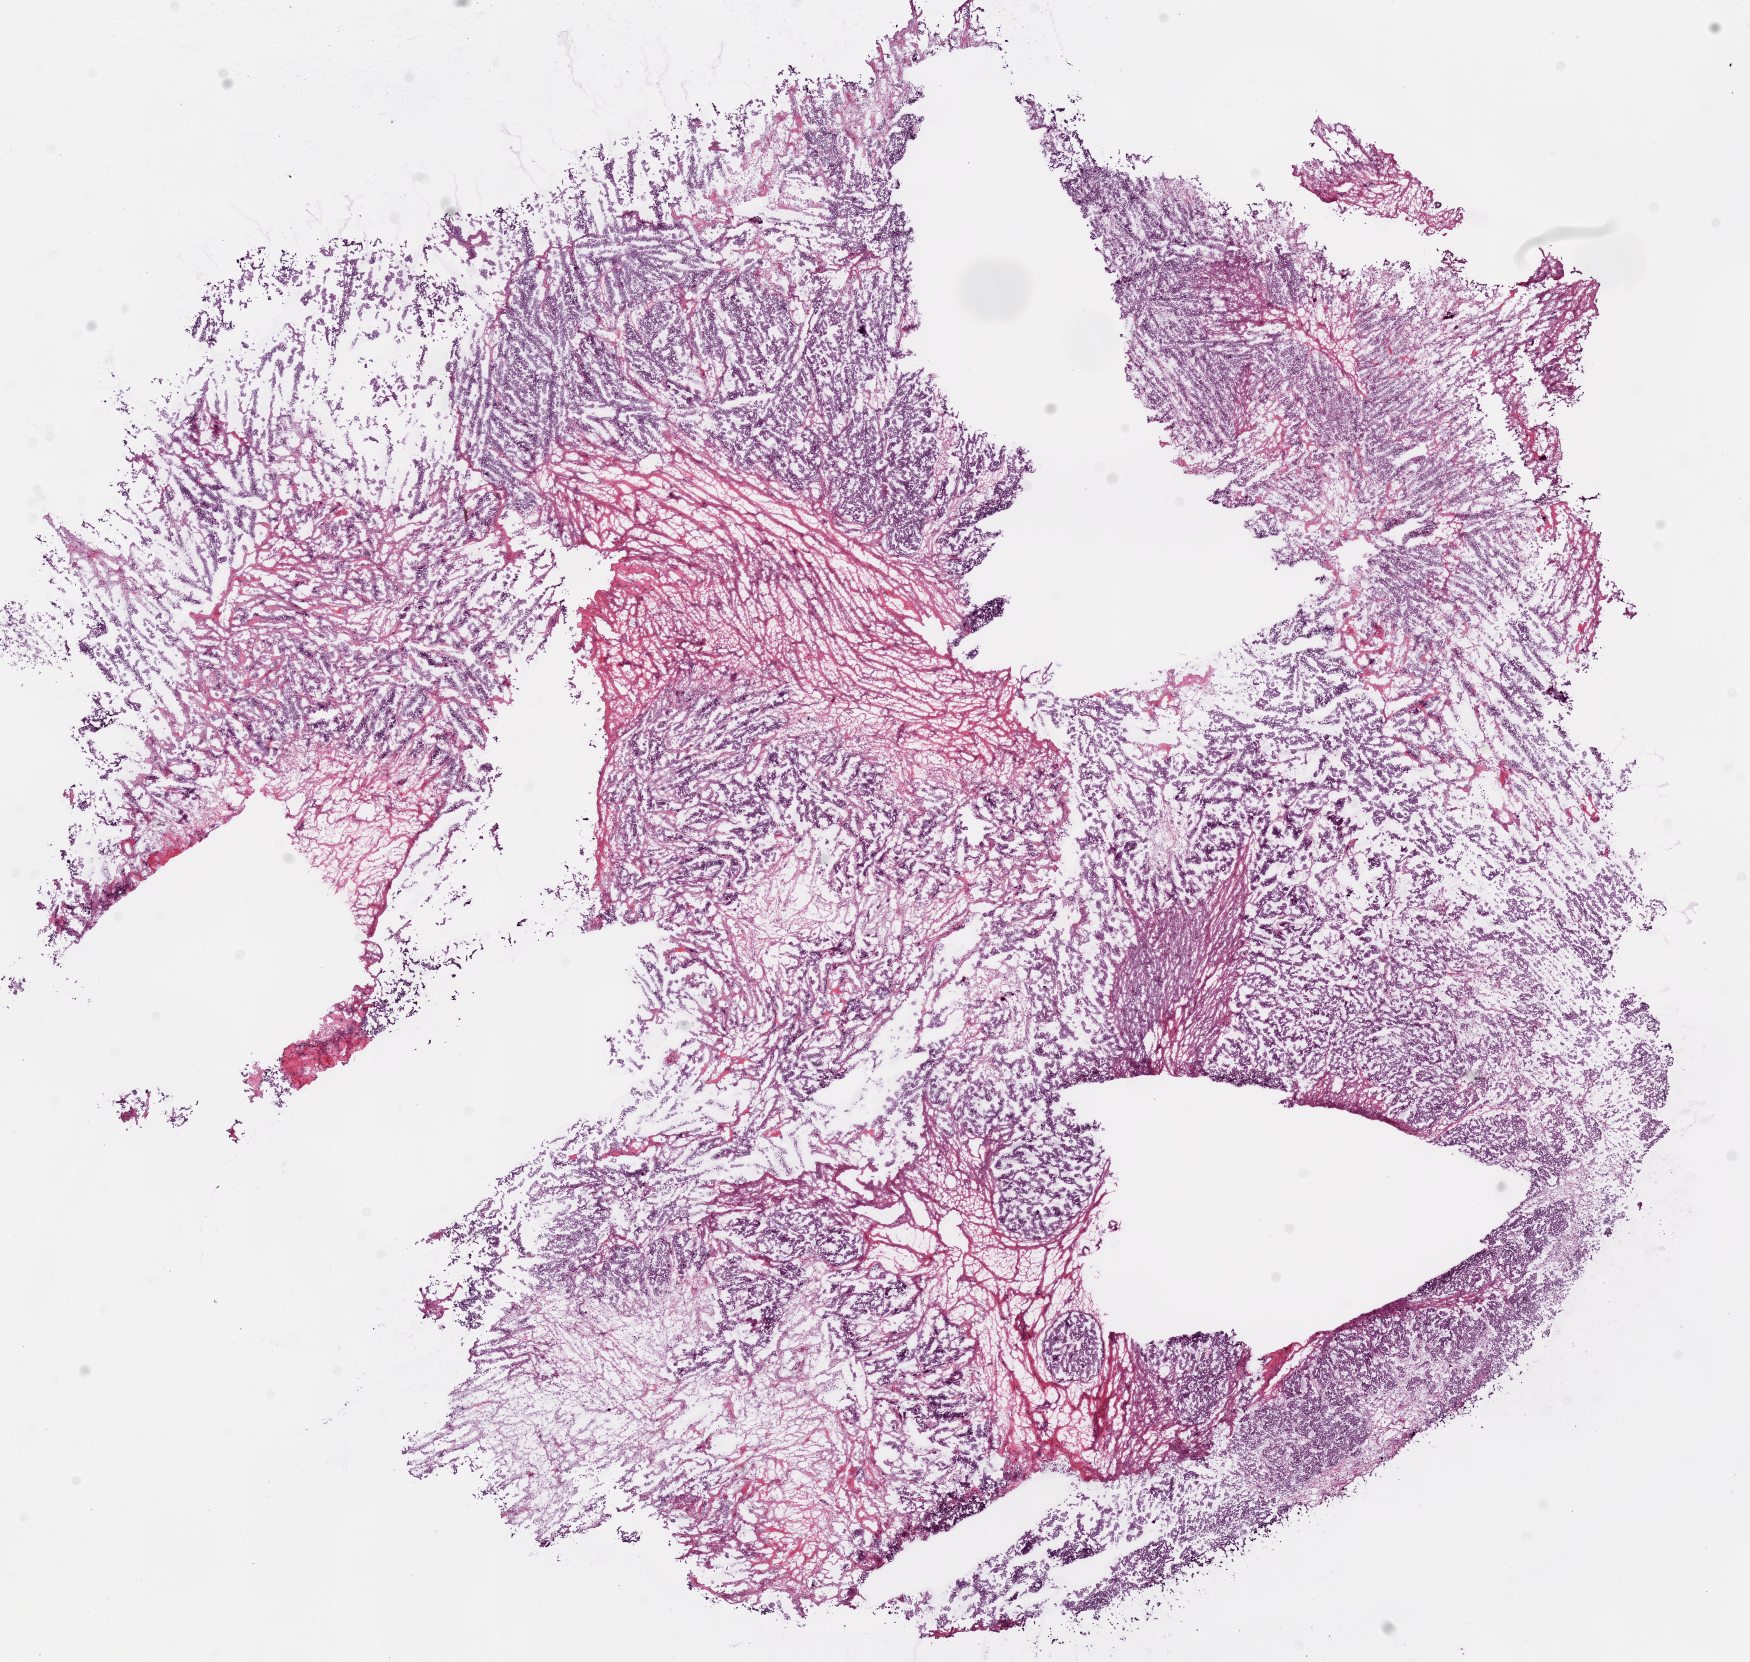
H&E whole-slide image — shown as a low-resolution overview of the whole scanned area (about 14.0 x 13.3 mm); frozen section from the bottom of the tissue portion; primary tumour sample from the ovary. Patient: female, age at initial diagnosis 49 years.
Histologic diagnosis: Serous cystadenocarcinoma, NOS.